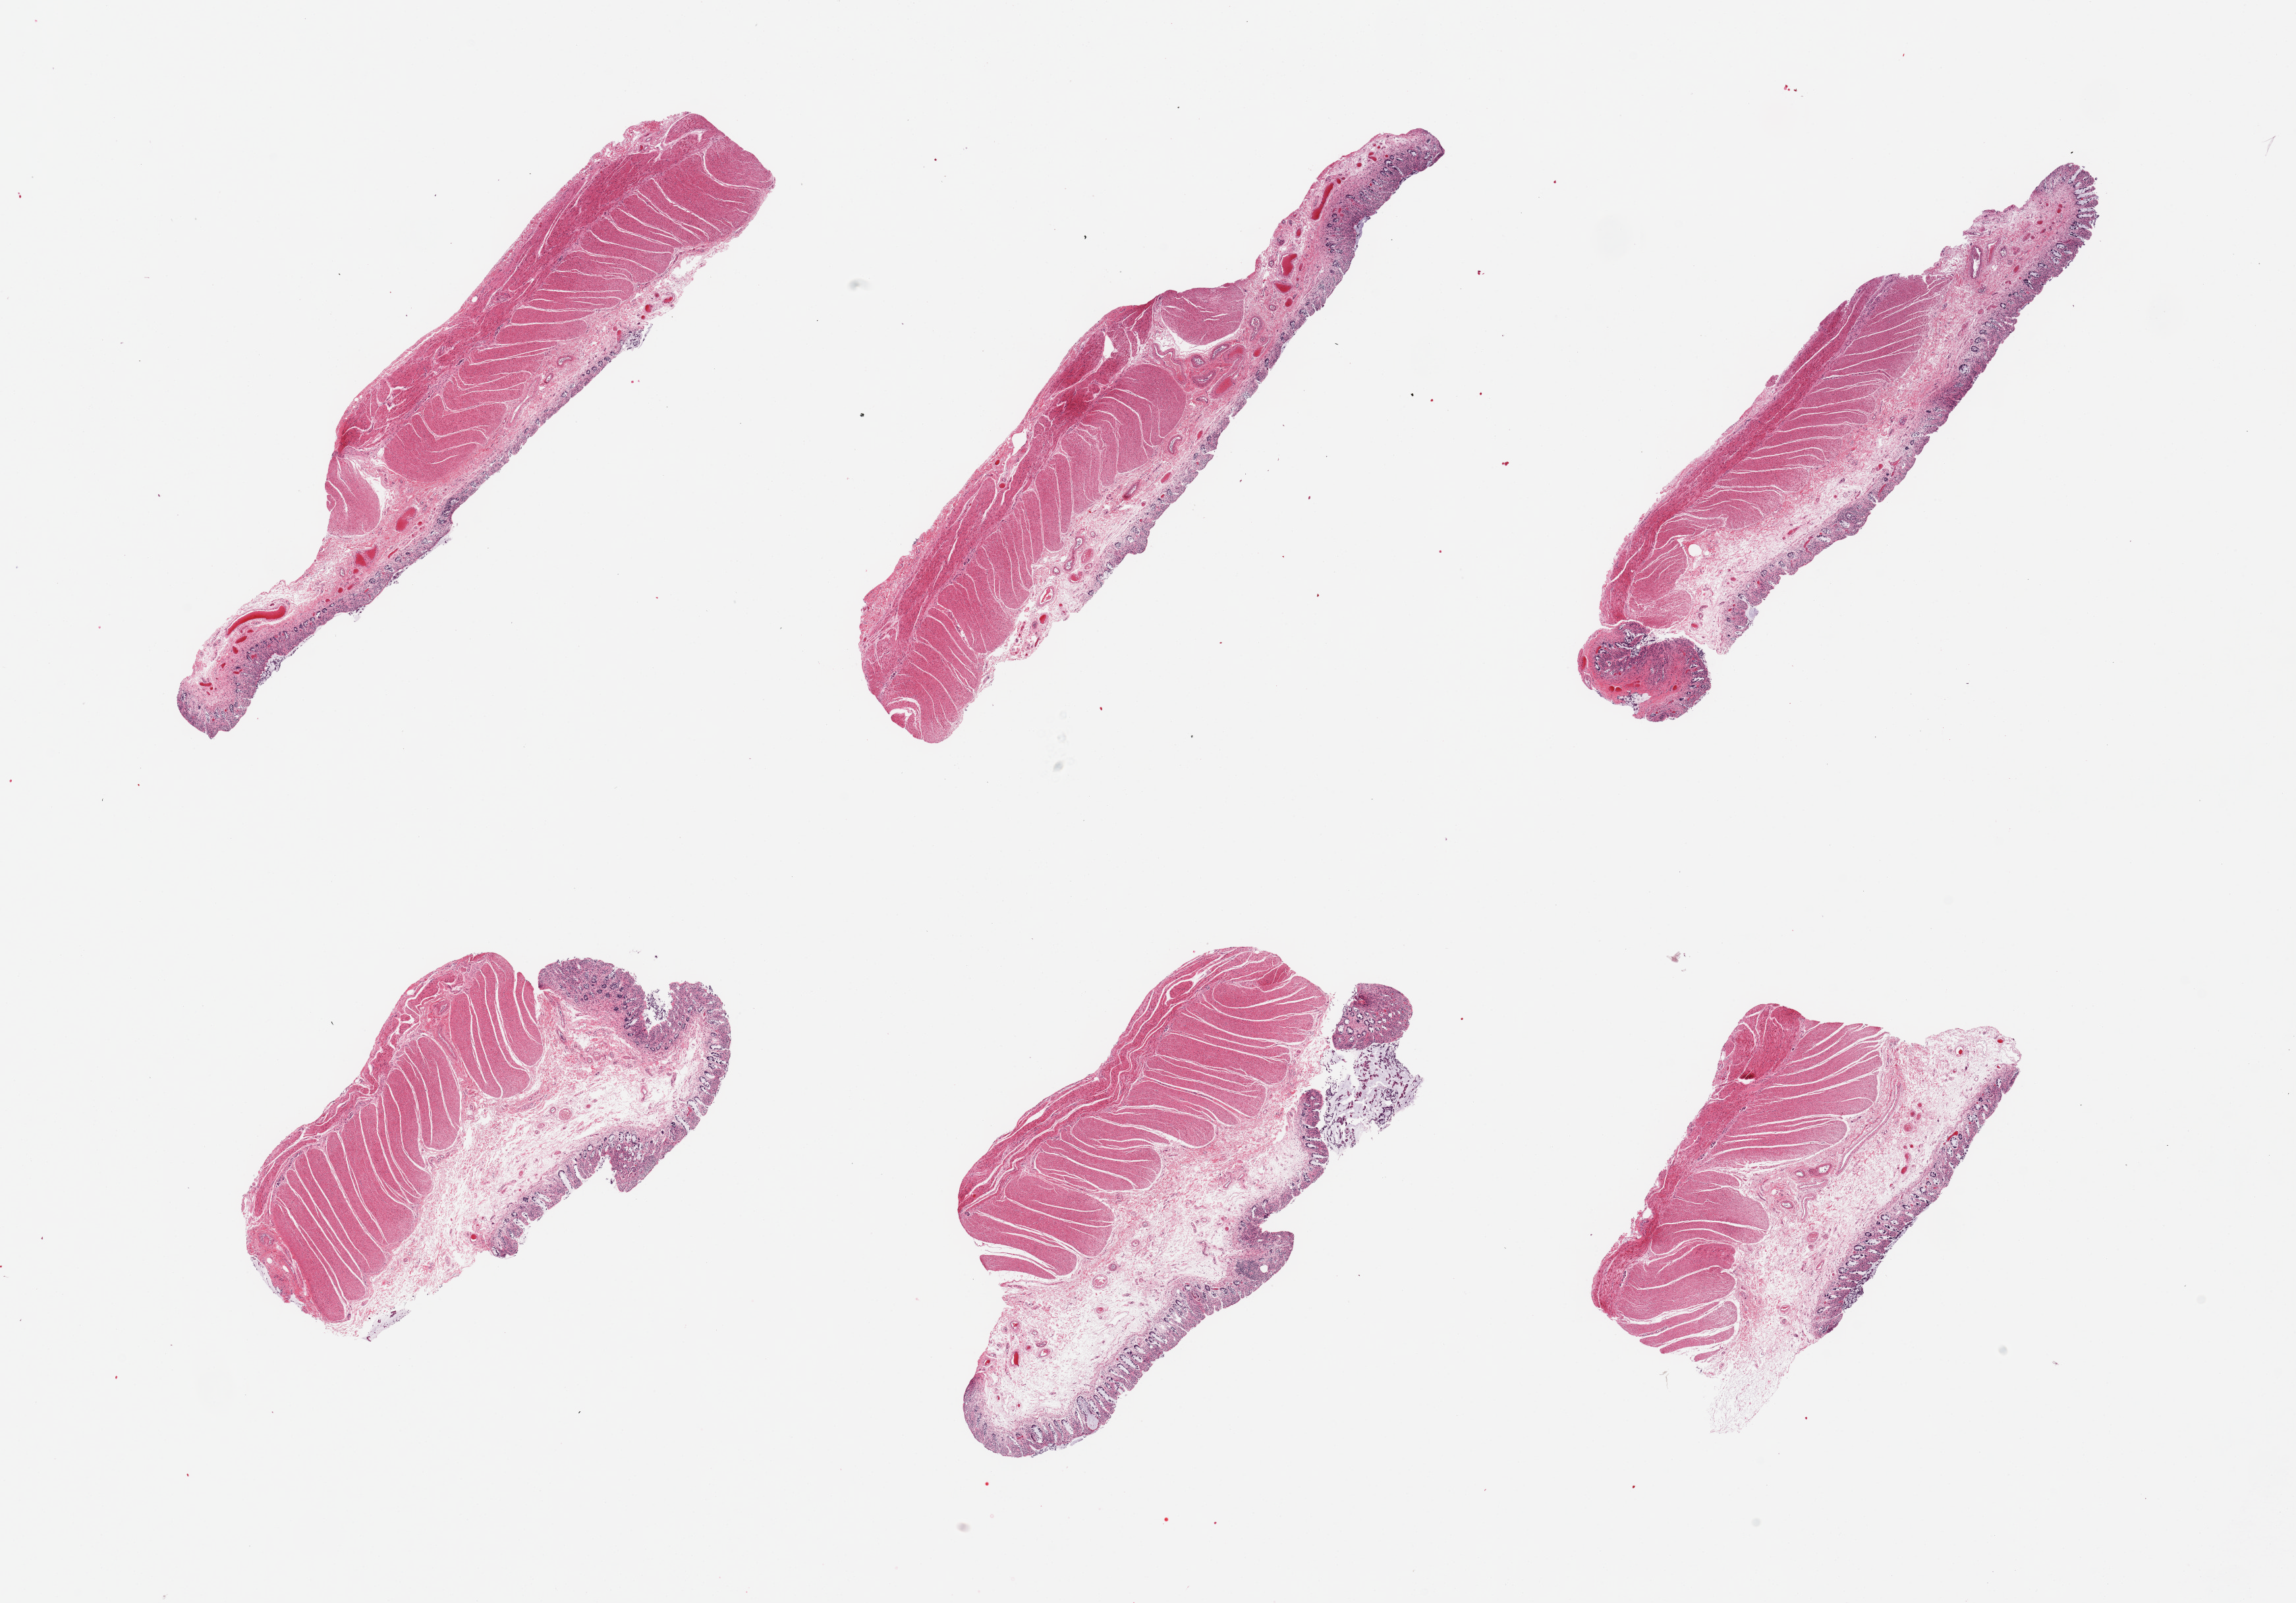
Digitized H&E-stained section, brightfield, whole scanned area (about 27.6 x 19.2 mm, from a 20x scan) shown as a low-resolution overview. PAXgene-fixed paraffin-embedded (PFPE) section. Sampled site (target tissue): transverse colon. Donor tissue sample. Donor: male.
* review note (as recorded): 6 pieces, mucosa ~10% thickness but totally autolyzed